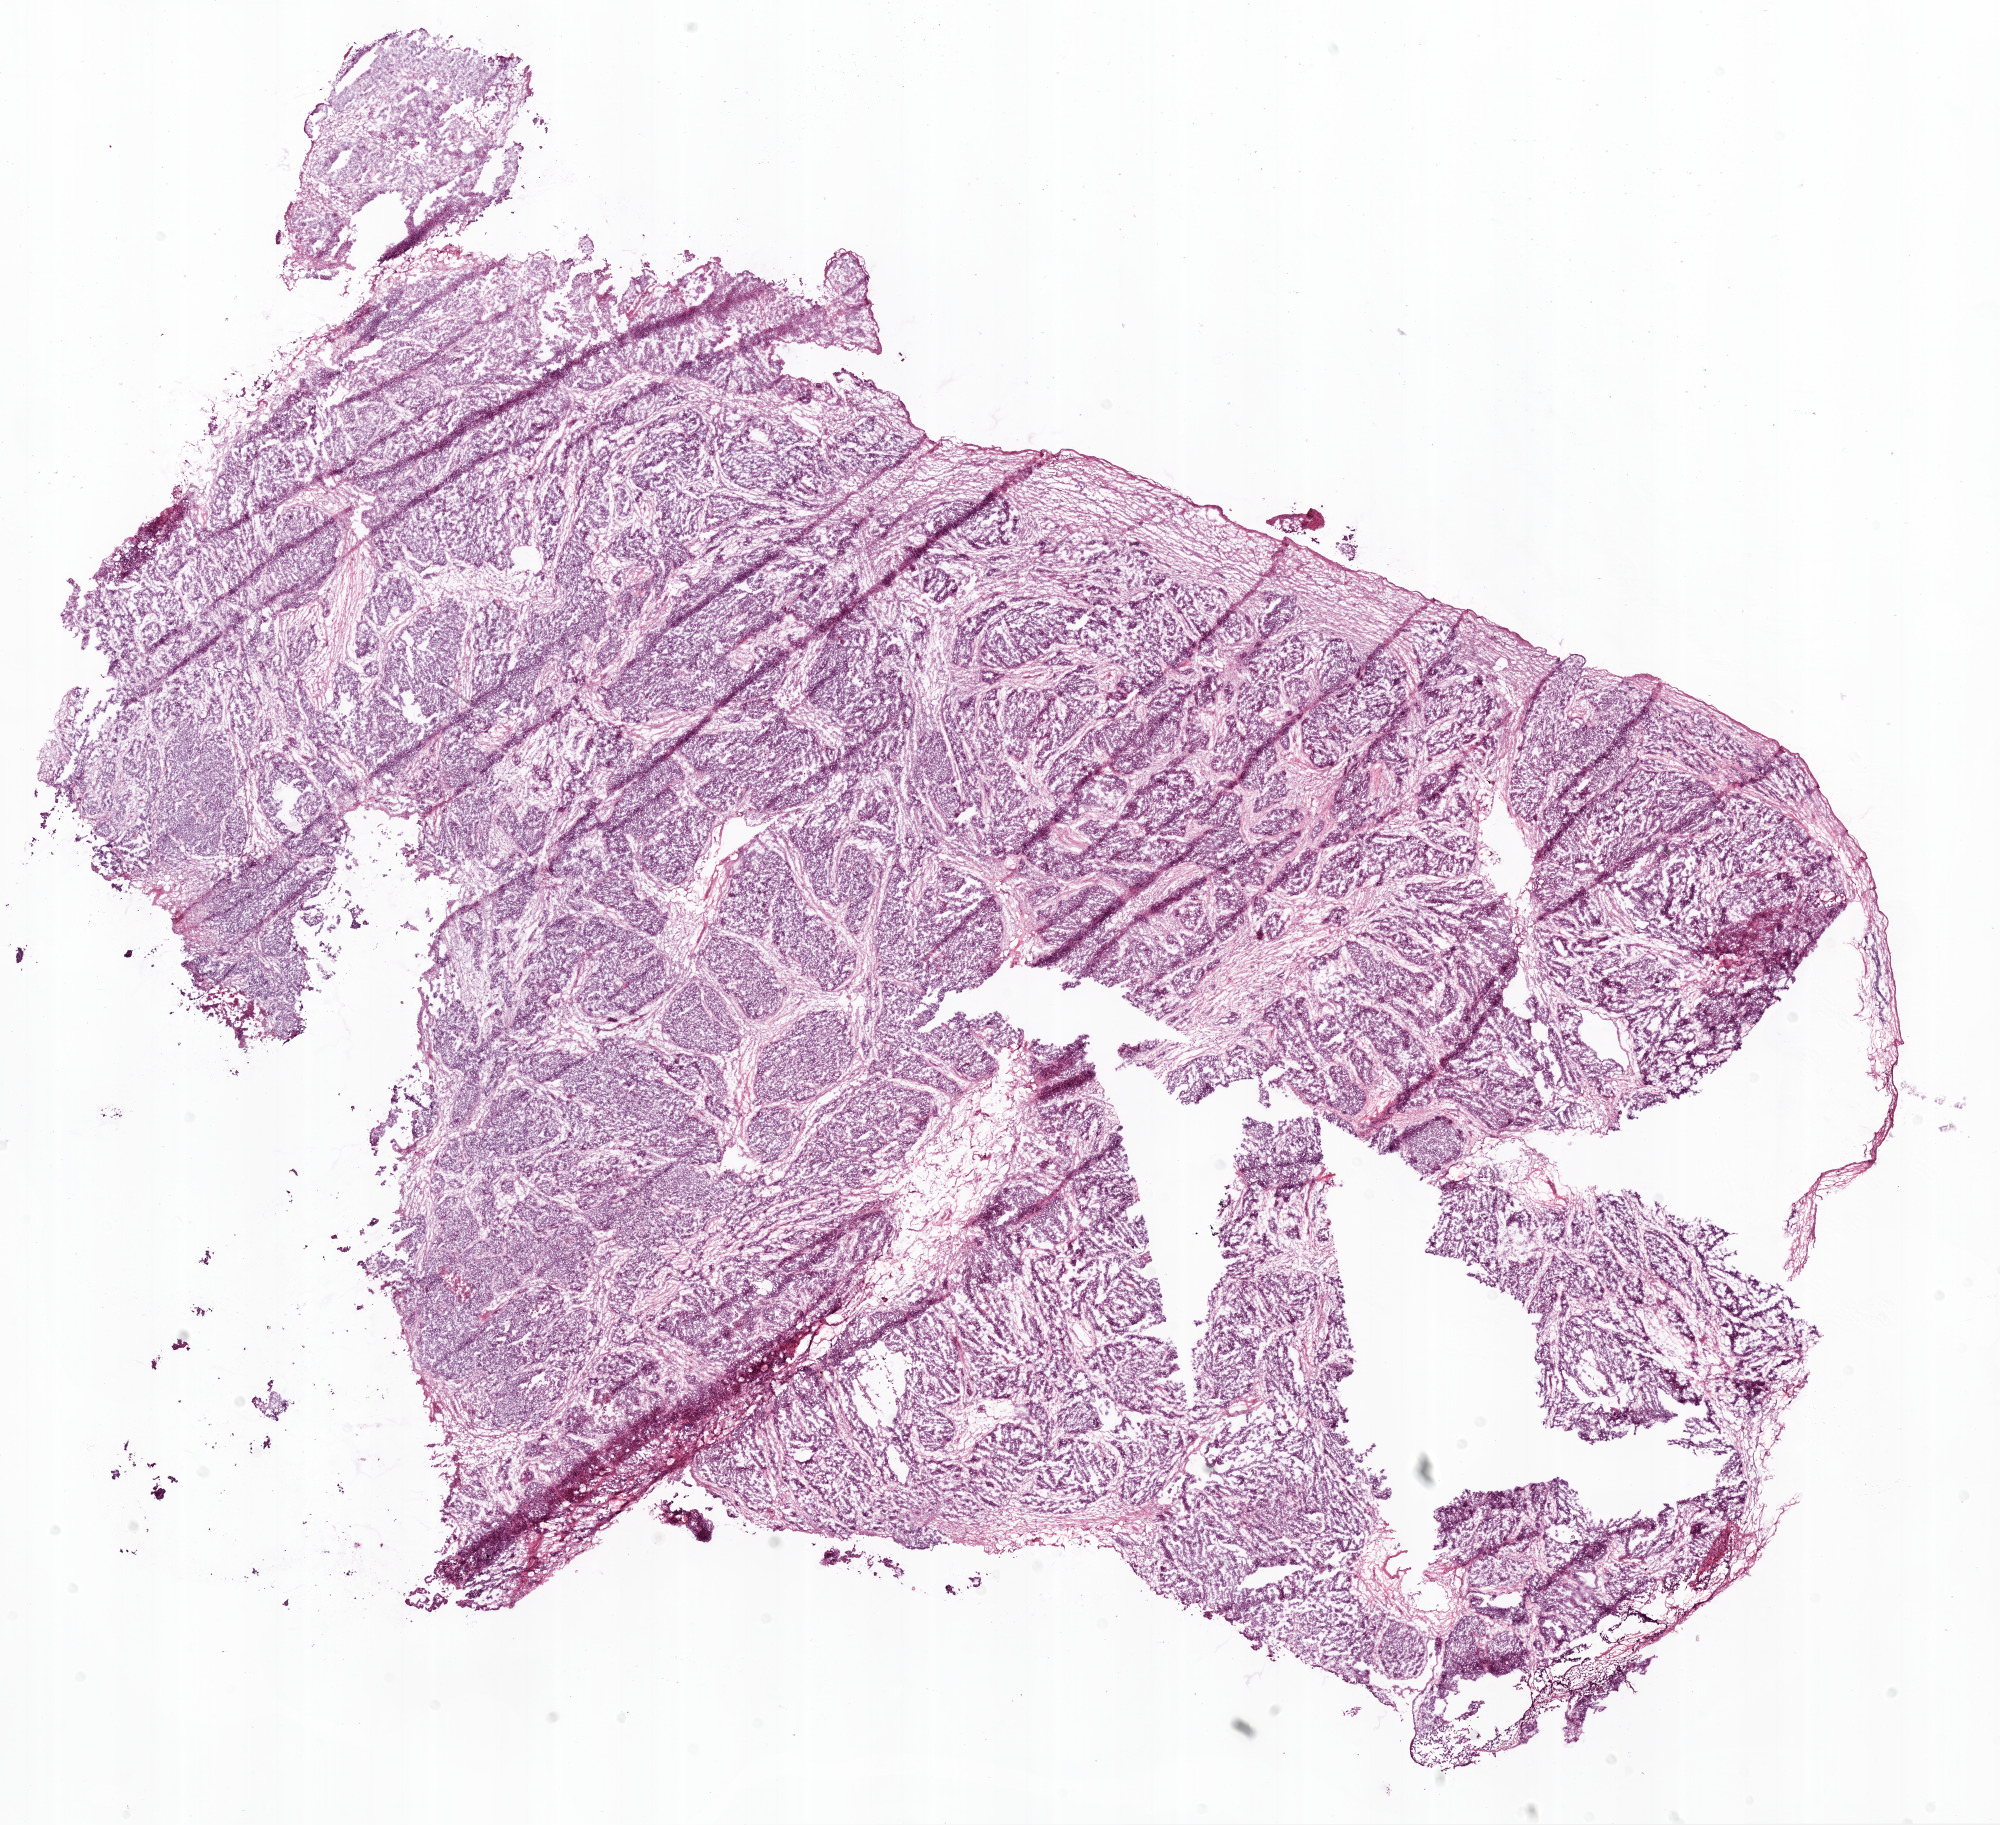
H&E-stained whole-slide image — whole scanned area (about 16.0 x 14.6 mm) shown as a low-resolution overview. Frozen section. Ovary, primary tumour sample. Female patient; age at initial diagnosis 39 years. Histologic grade: G2 (moderately differentiated). Pathologist review of this section (percent, as recorded): tumour cells 100%, tumour nuclei 80%, normal cells 0%, stromal cells 0%, necrosis 0%.
FIGO stage: IIIC. Laterality: bilateral. Histologic diagnosis: Serous cystadenocarcinoma, NOS.